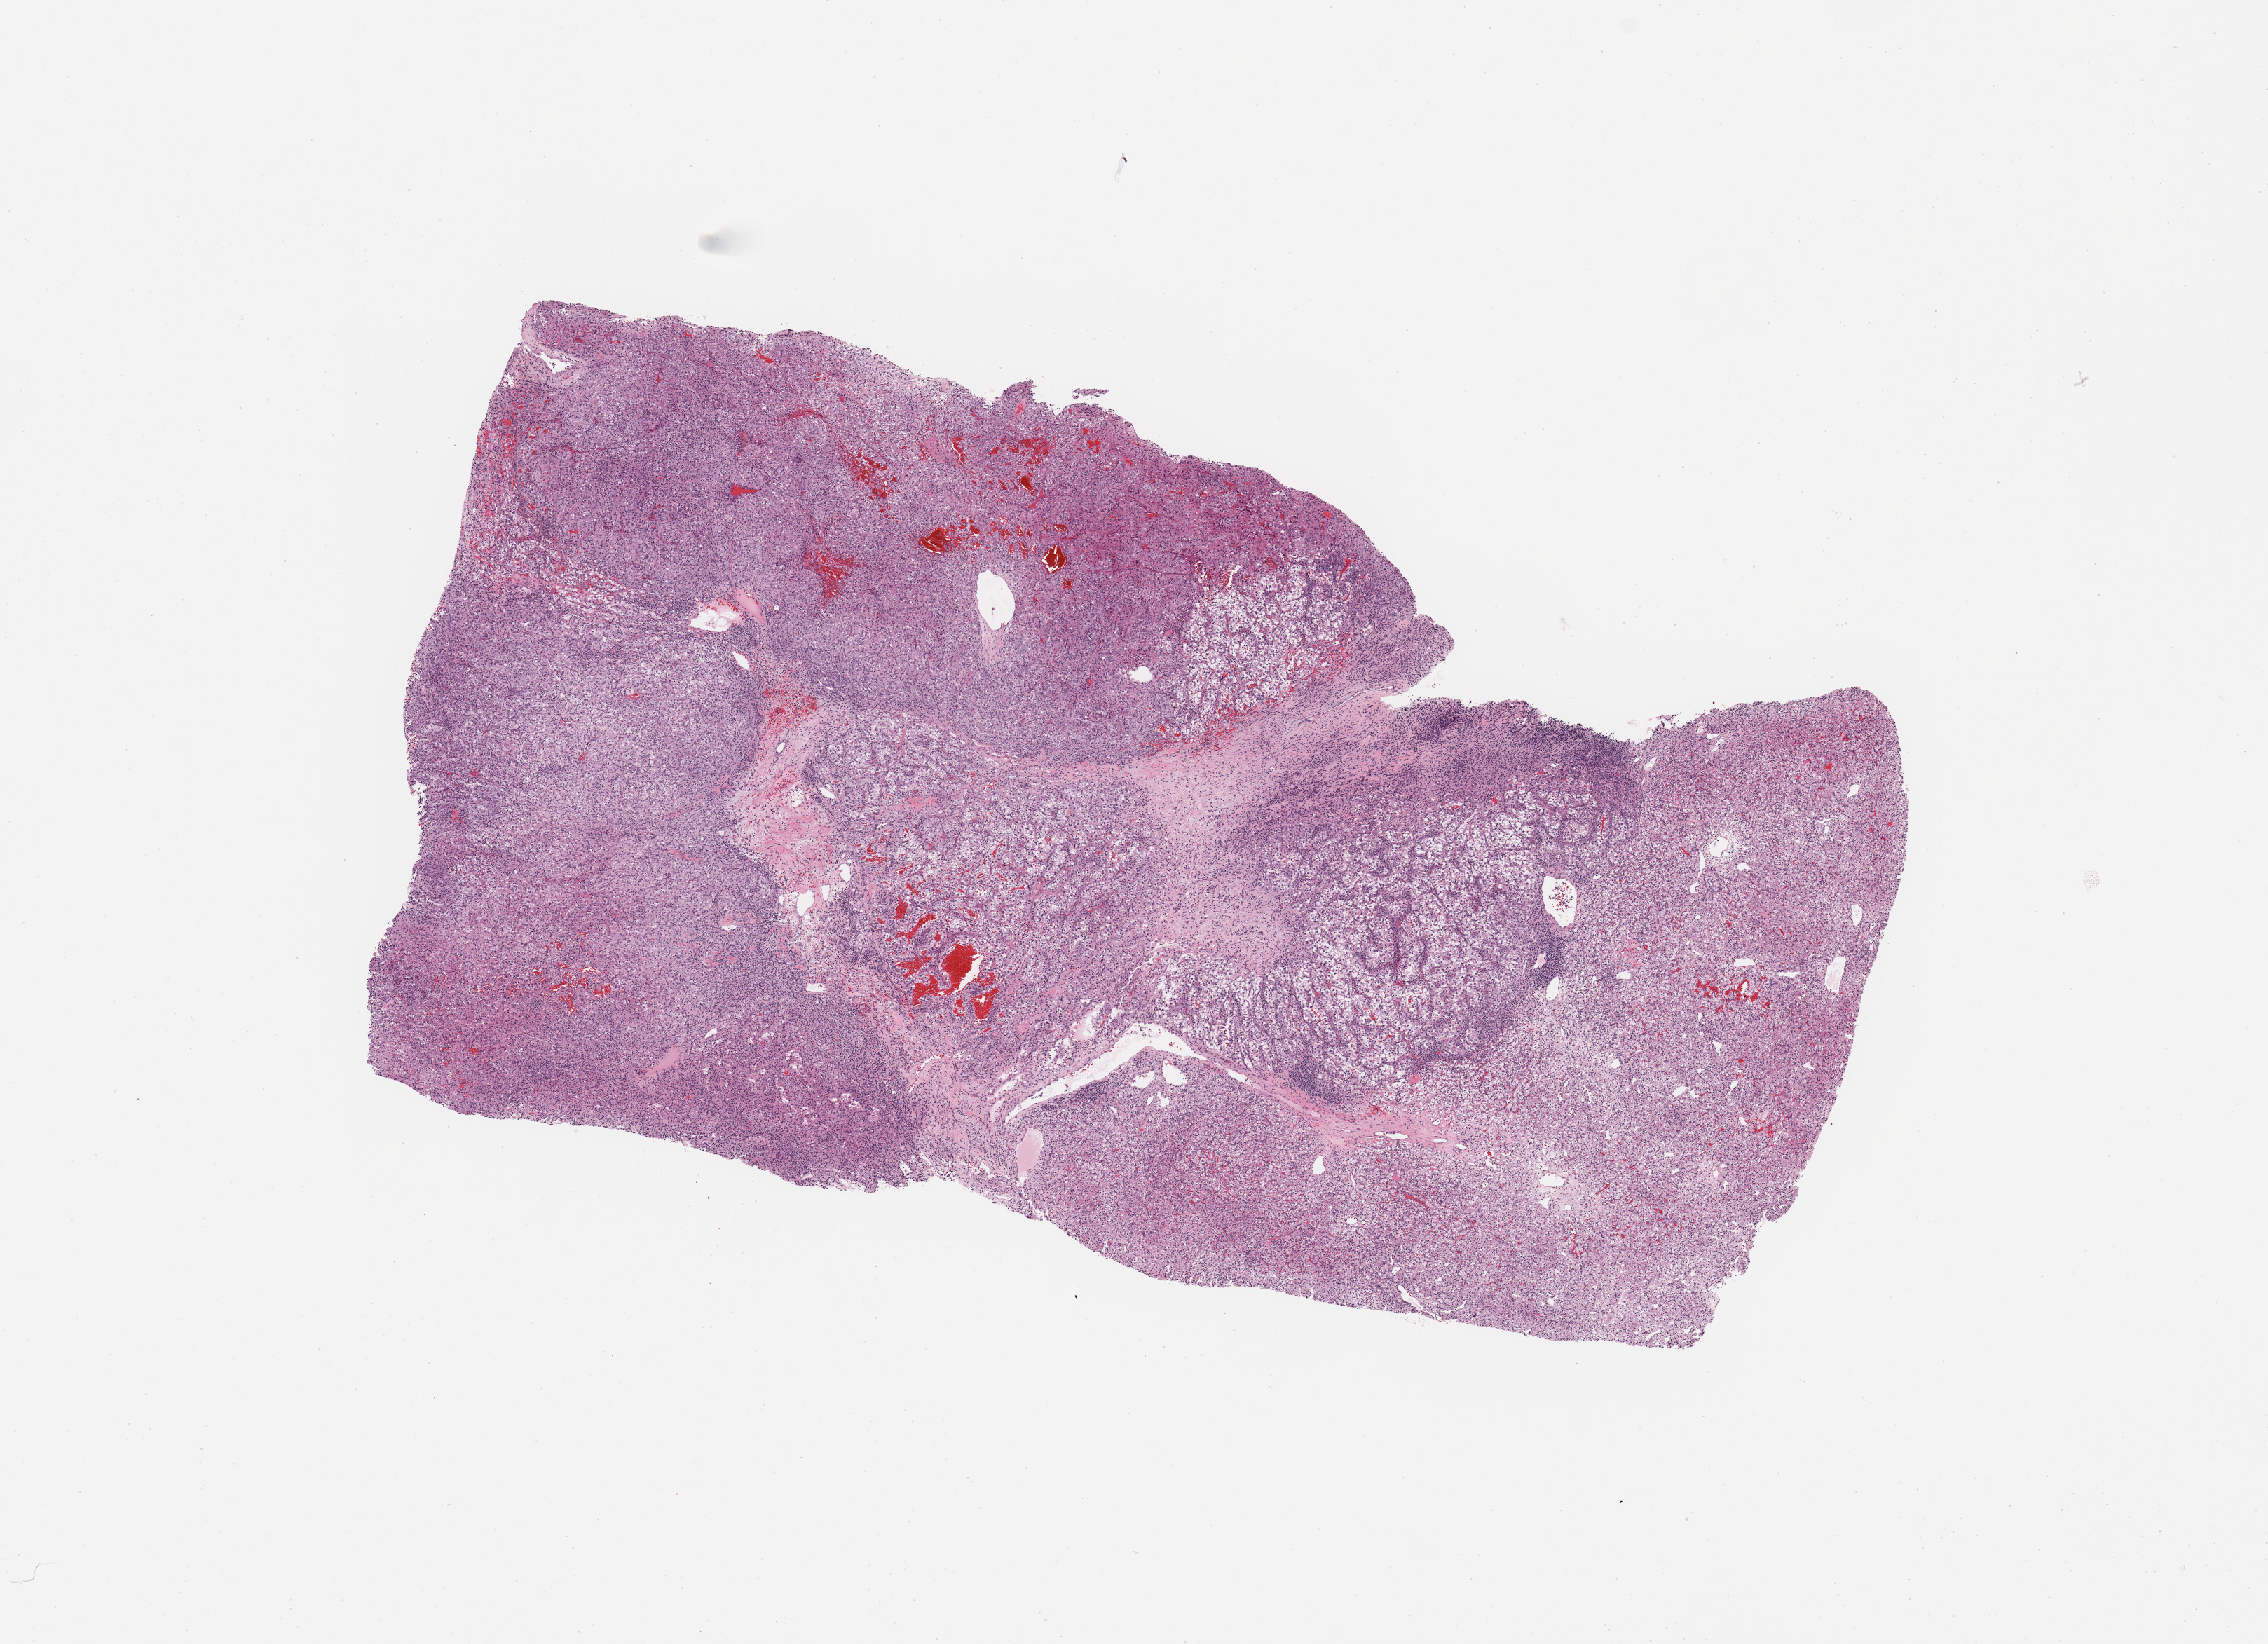
Whole-slide histology image, H&E, whole scanned area (about 12.8 x 9.3 mm, slide scanned at 20x) shown as a low-resolution overview. Tumour tissue sample, sampled site: kidney. Patient: male, age 62 years. Histologic grade: G4 (undifferentiated). Slide review estimates, as recorded: tumour nuclei 85%, necrosis 5%.
AJCC pathologic stage: III. Histologic diagnosis: Renal cell carcinoma, NOS.